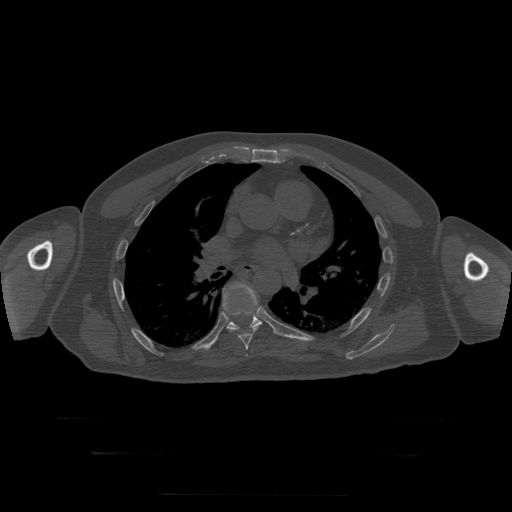
CT including the spine, one axial slice; slice 178 of 397 in the series (ordered by position); reconstruction kernel STANDARD; bone window (W 1800 / L 400 HU); 1.25 mm slice thickness; 512 × 512 image matrix. Patient age 73 years. Case-level facts recorded for this patient, not image findings: primary cancer: prostate.
Annotated regions visible in this slice (semi-automatic segmentation, software-assisted and operator-edited):
- T7 vertebra: bounding box [x1, y1, x2, y2] px = [227, 312, 257, 351]
- T8 vertebra: [215, 283, 263, 342]